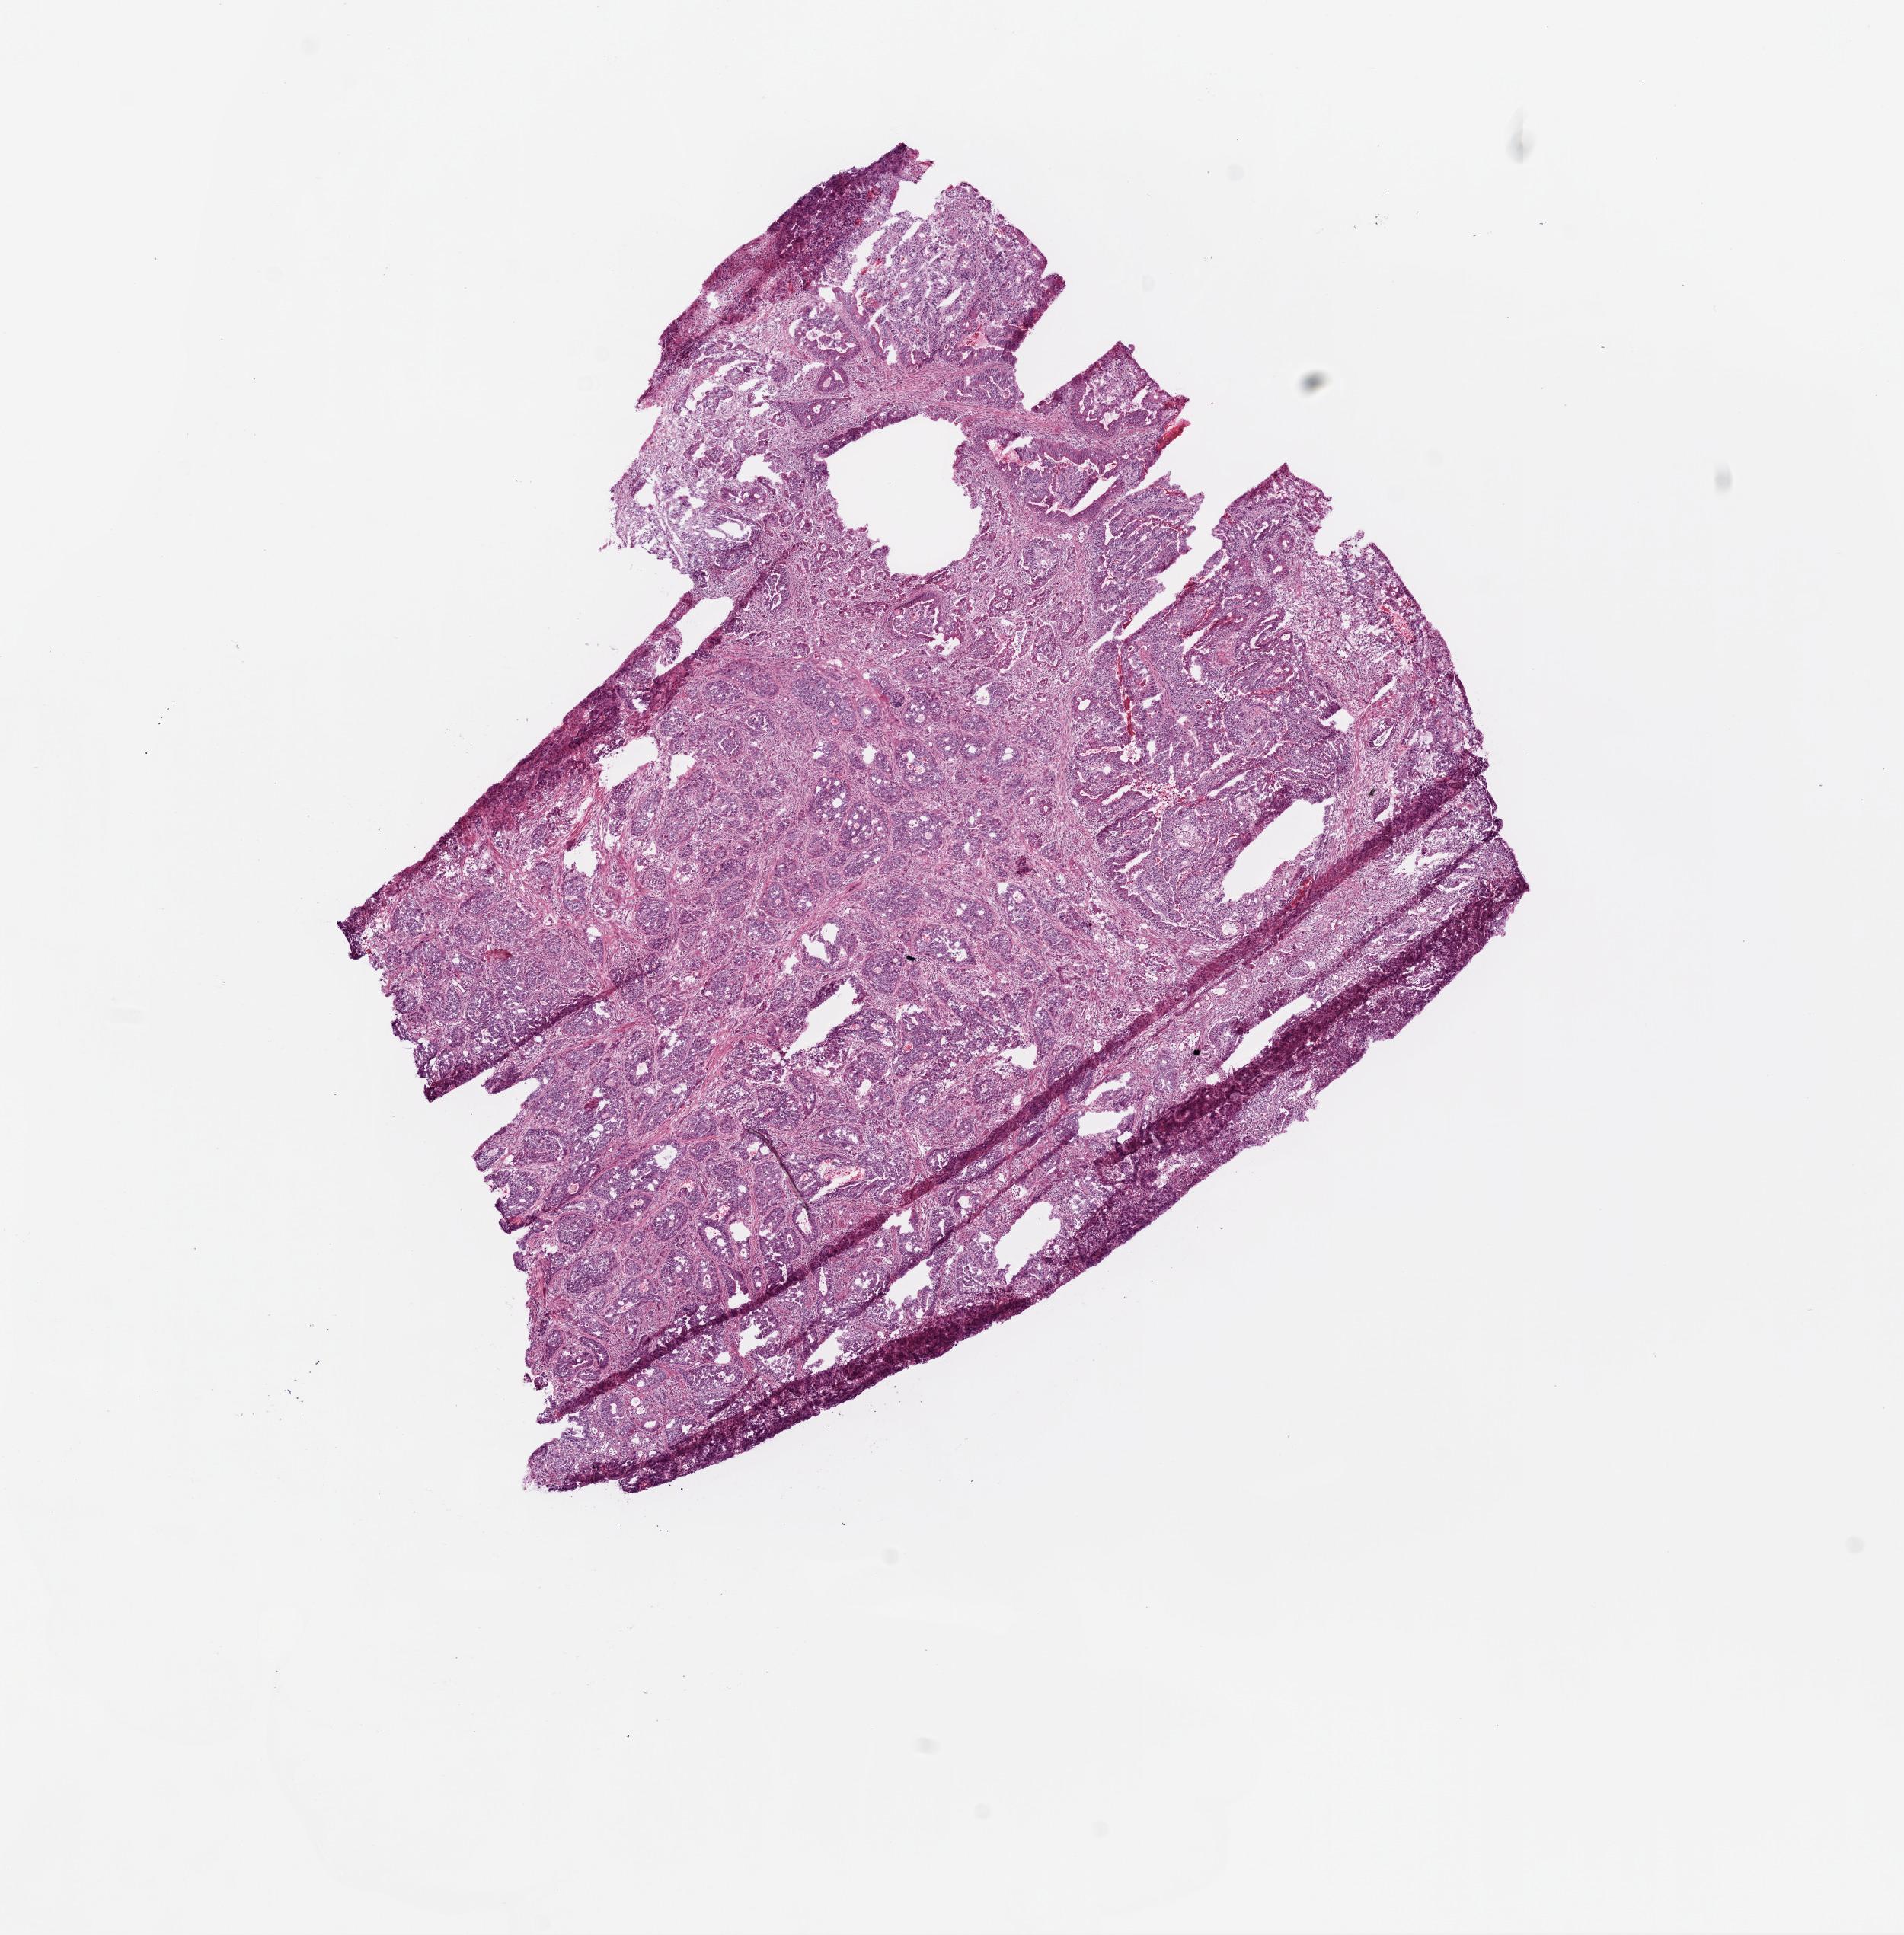
Hematoxylin and eosin (H&E) stained whole-slide image — shown as a low-resolution overview of the whole scanned area (about 10.0 x 10.2 mm); frozen section from the top of the tissue portion; sample: primary tumour, colon. Female, age 54 years at initial diagnosis. Composition of this section per pathologist review: tumour cells 70%, tumour nuclei 90%, normal cells 0%, stromal cells 29%, necrosis 1%.
* AJCC pathologic stage: I (6th edition)
* diagnosis: Adenocarcinoma, NOS (sigmoid colon)